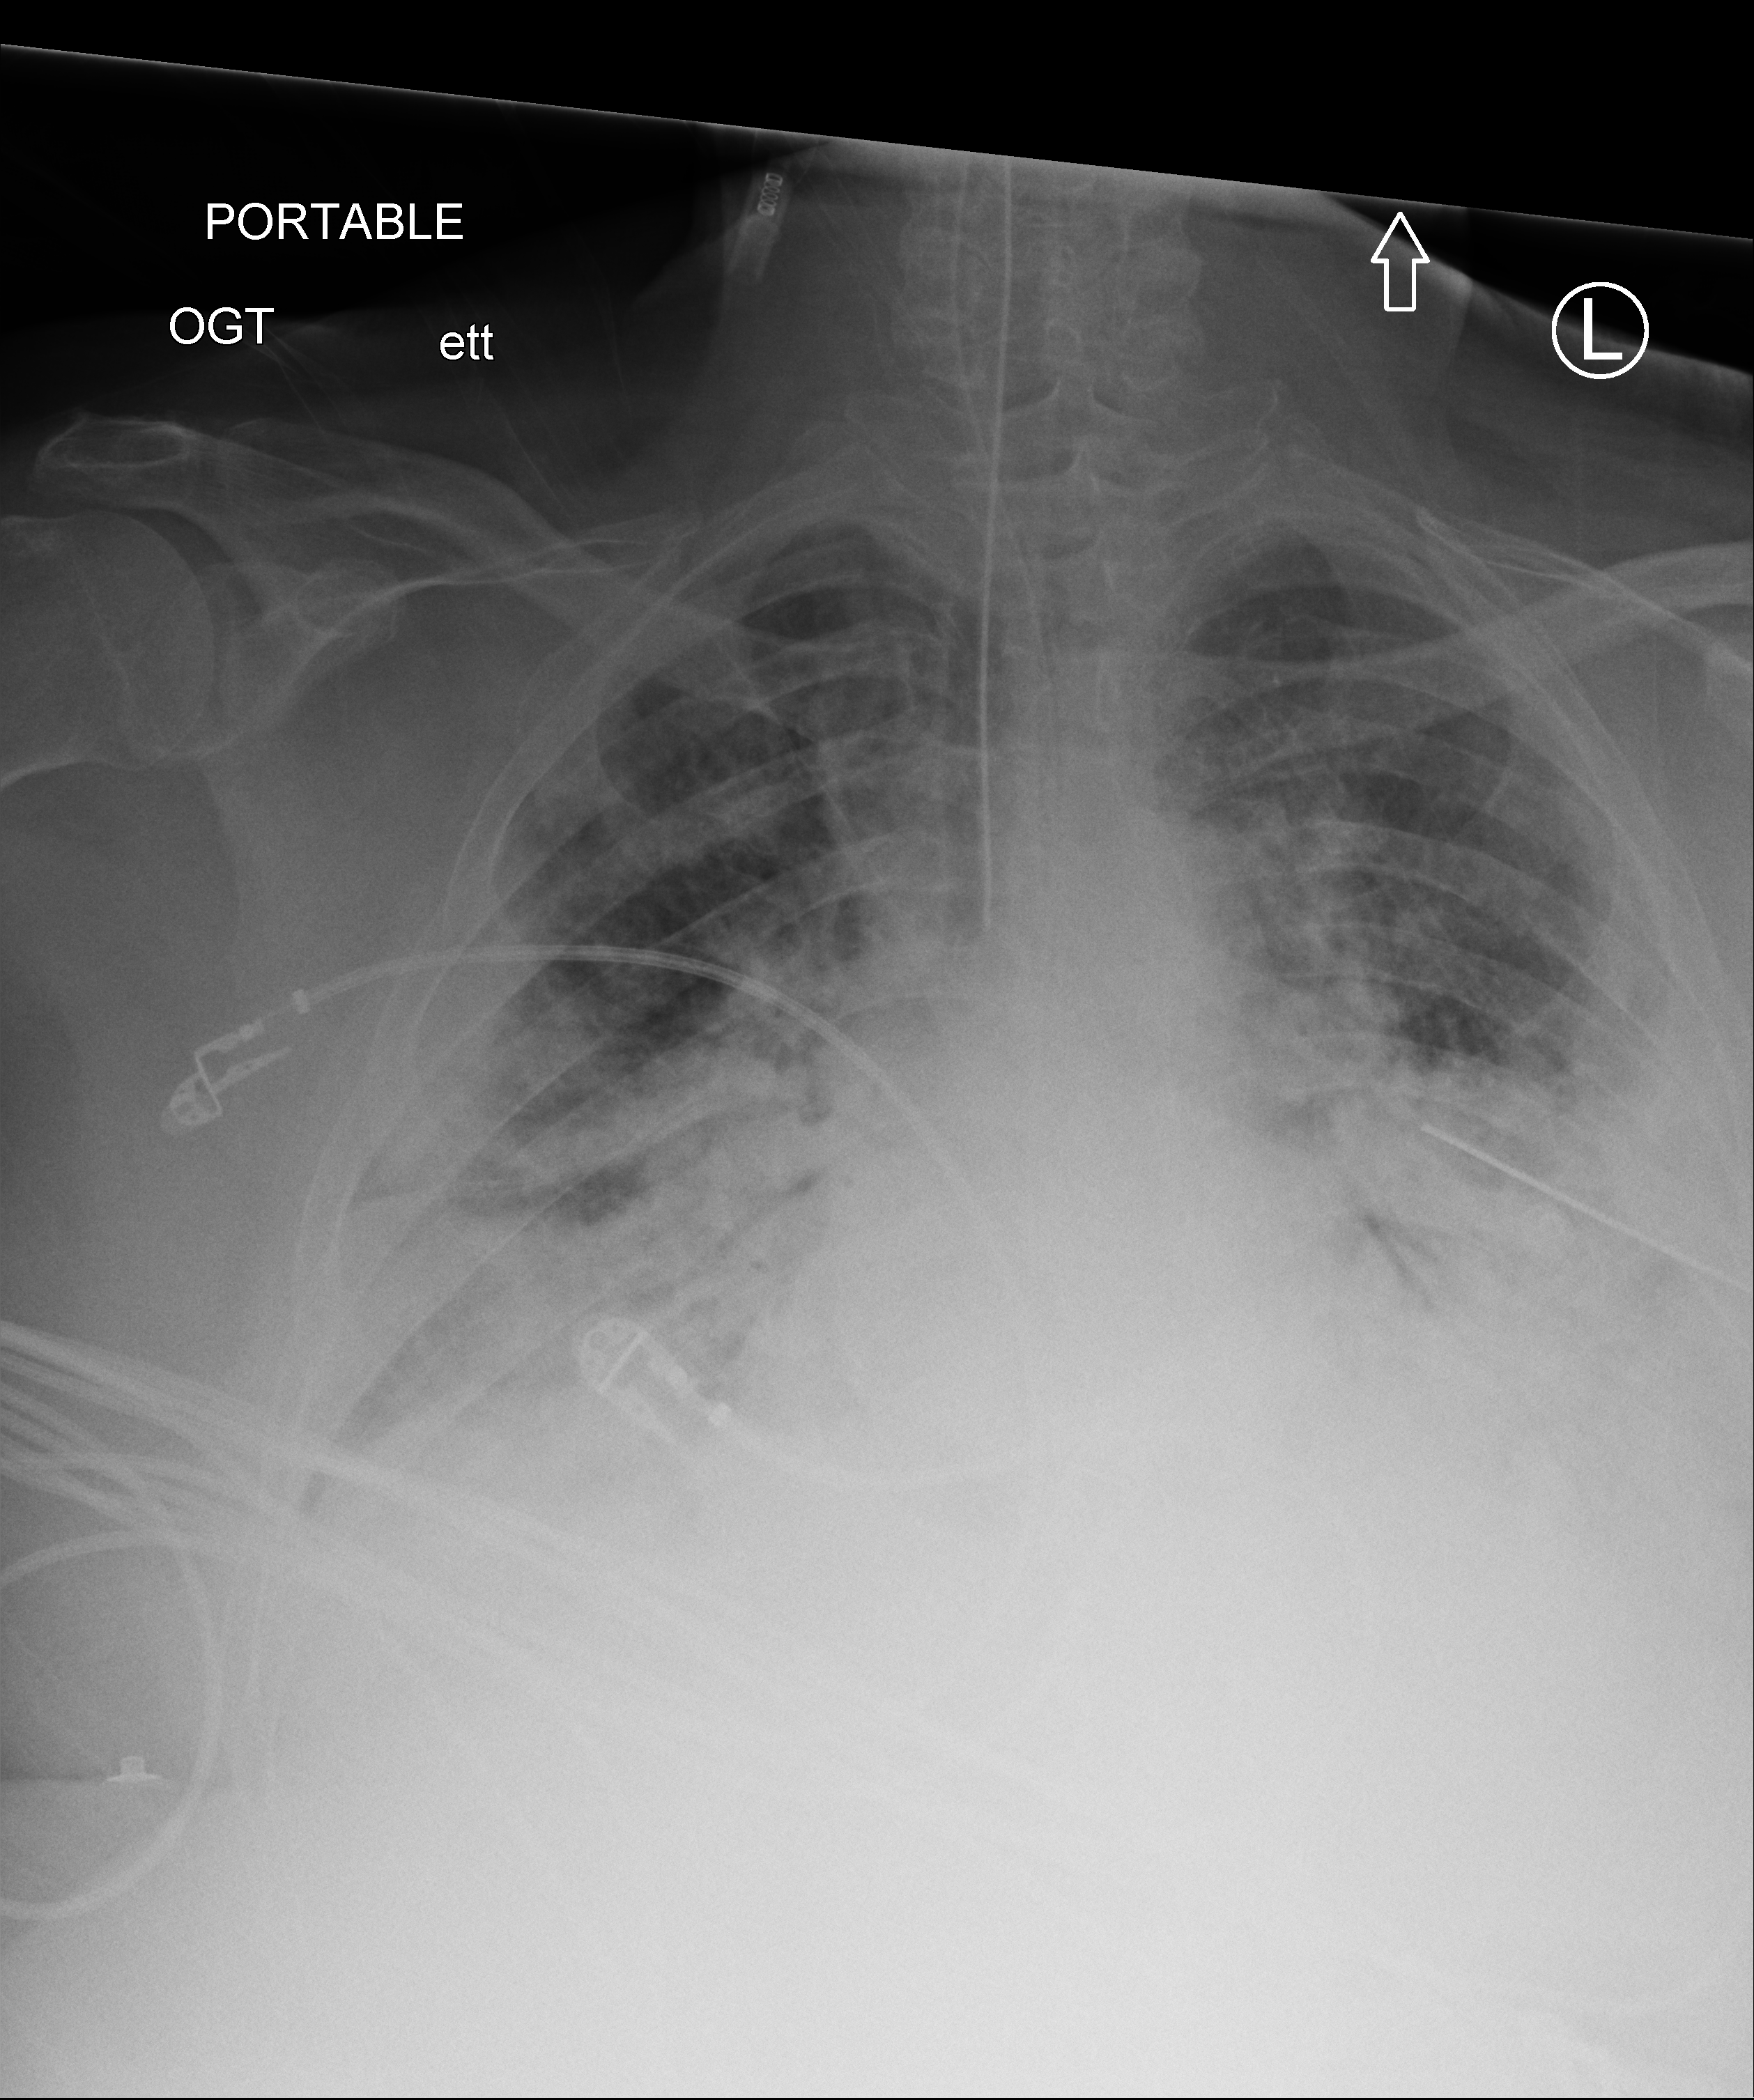
Chest X-ray (portable); anteroposterior (AP) projection. Male patient hospitalised with COVID-19, age 60–74 years.
Admission-level facts for this patient (not findings on this image; timing relative to this image not recorded): hypertension (admission record): yes; admitted to intensive care during this hospital stay: yes; mechanically ventilated during this hospital stay: yes.